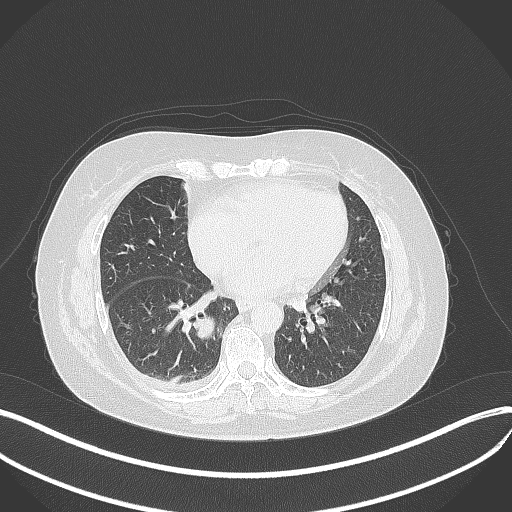
Chest CT, one axial slice. Slice 145 of 381 in the series (ordered by position). Lung window (W 1500 / L -600 HU). 1 mm slice thickness. 512 × 512 image matrix, field of view 400 × 400 mm. Female patient, age 56 years. From the clinical record (not read from this slice): clinical TNM (as recorded): T2b N1 M0; histopathological grade: G3.
Outlined on this slice (rectangle marked by the reading radiologist):
- lung tumour (recorded histology: small cell carcinoma): box from (x=194, y=315) to (x=219, y=344) px